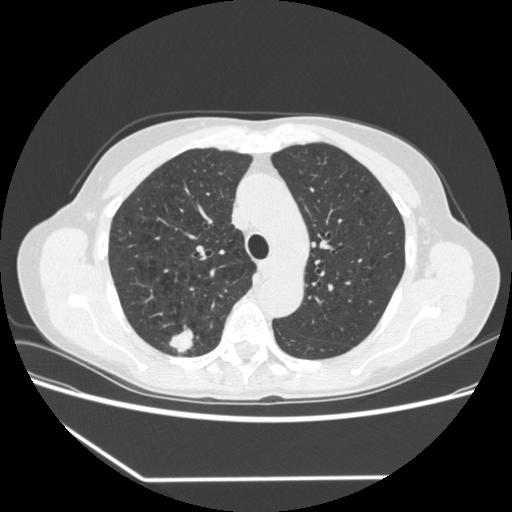
Low-dose screening chest CT, one axial slice; position 240 of 323 along the scan axis; reconstruction kernel STANDARD; 120 kVp; lung window (W 1500 / L -600 HU); 1.25 mm slice thickness; 512 × 512 image matrix, field of view 360 × 360 mm.
Outlined on this slice (outlined manually by an expert reader):
- lesion 1 (tumor, upper lobe of right lung): bounding box [x1, y1, x2, y2] px = [169, 325, 198, 354]